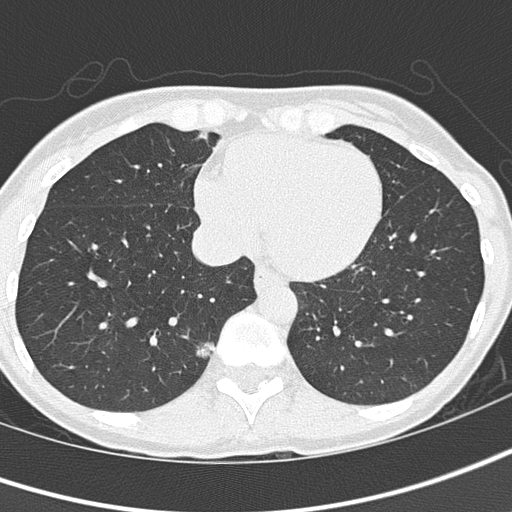
Low-dose screening chest CT, axial slice; baseline annual screen; lung window (W 1500 / L -600 HU); 120 kVp; slice 100 of 145 in the series; 512 × 512 image matrix. Female, age 57 years at enrolment. Current smoker at enrolment.
• Expert-annotated lung lesion, bounding box <181,337,219,366> (left, top, right, bottom; pixels).
• Screening reader's record for this exam (one nodule recorded; not confirmed to be the boxed lesion): non-calcified nodule or mass ≥4 mm, right lower lobe, 11 × 6 mm, mixed attenuation.
• Later outcome: lung cancer diagnosed 61 days after this screen — adenocarcinoma, NOS, right lower lobe, moderately differentiated (G2), stage IA (AJCC 6th edition), 8 mm at pathology.